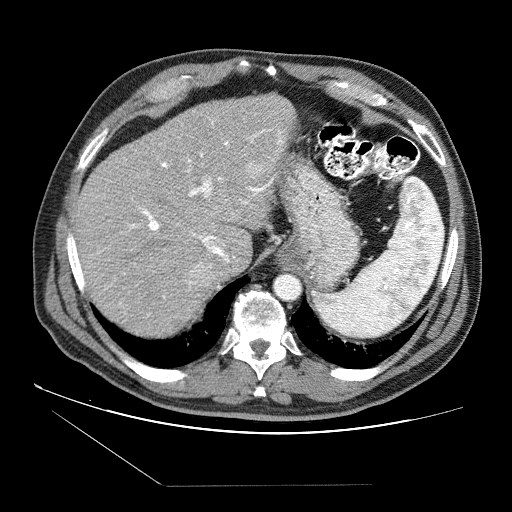
Contrast-enhanced abdominal CT (liver protocol), one axial slice. Position 61 of 87 along the scan axis. Reconstruction kernel STANDARD. 120 kVp. Soft-tissue window (W 400 / L 40 HU). 512 × 512 image matrix. Case-level facts recorded for this patient, not image findings: diagnosis: hepatocellular carcinoma (patient treated with transarterial chemoembolisation; whether this scan precedes or follows treatment is not stated here); TNM stage (as recorded): Stage-II; Child-Pugh class: B.
Annotated regions visible in this slice (semi-automatically segmented with operator editing):
- liver parenchyma outside the tumour (the mass and vessels are separate outlines, so this box may not span the whole liver): bounding box <76,92,296,336> (left, top, right, bottom; pixels)
- mass: <190,161,263,287>
- liver vessels: <90,121,283,317>